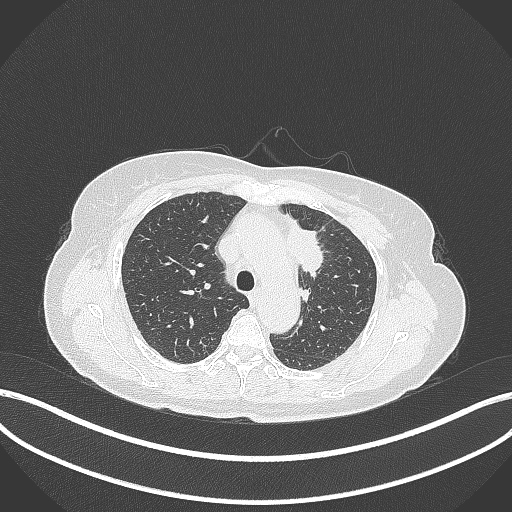
Chest CT, one axial slice; reconstruction kernel B70f; lung window (W 1500 / L -600 HU); 1 mm slice thickness; 512 × 512 image matrix, field of view 400 × 400 mm. Female patient, age 65 years. Case-level facts recorded for this patient, not image findings: clinical TNM (as recorded): T2a N0 M0; histopathological grade: G2-3.
Structures marked on this image (bounding box drawn by a radiologist):
- lung tumour (recorded histology: adenocarcinoma): bounding box (x1, y1, x2, y2) in pixels: (284, 218, 326, 279)